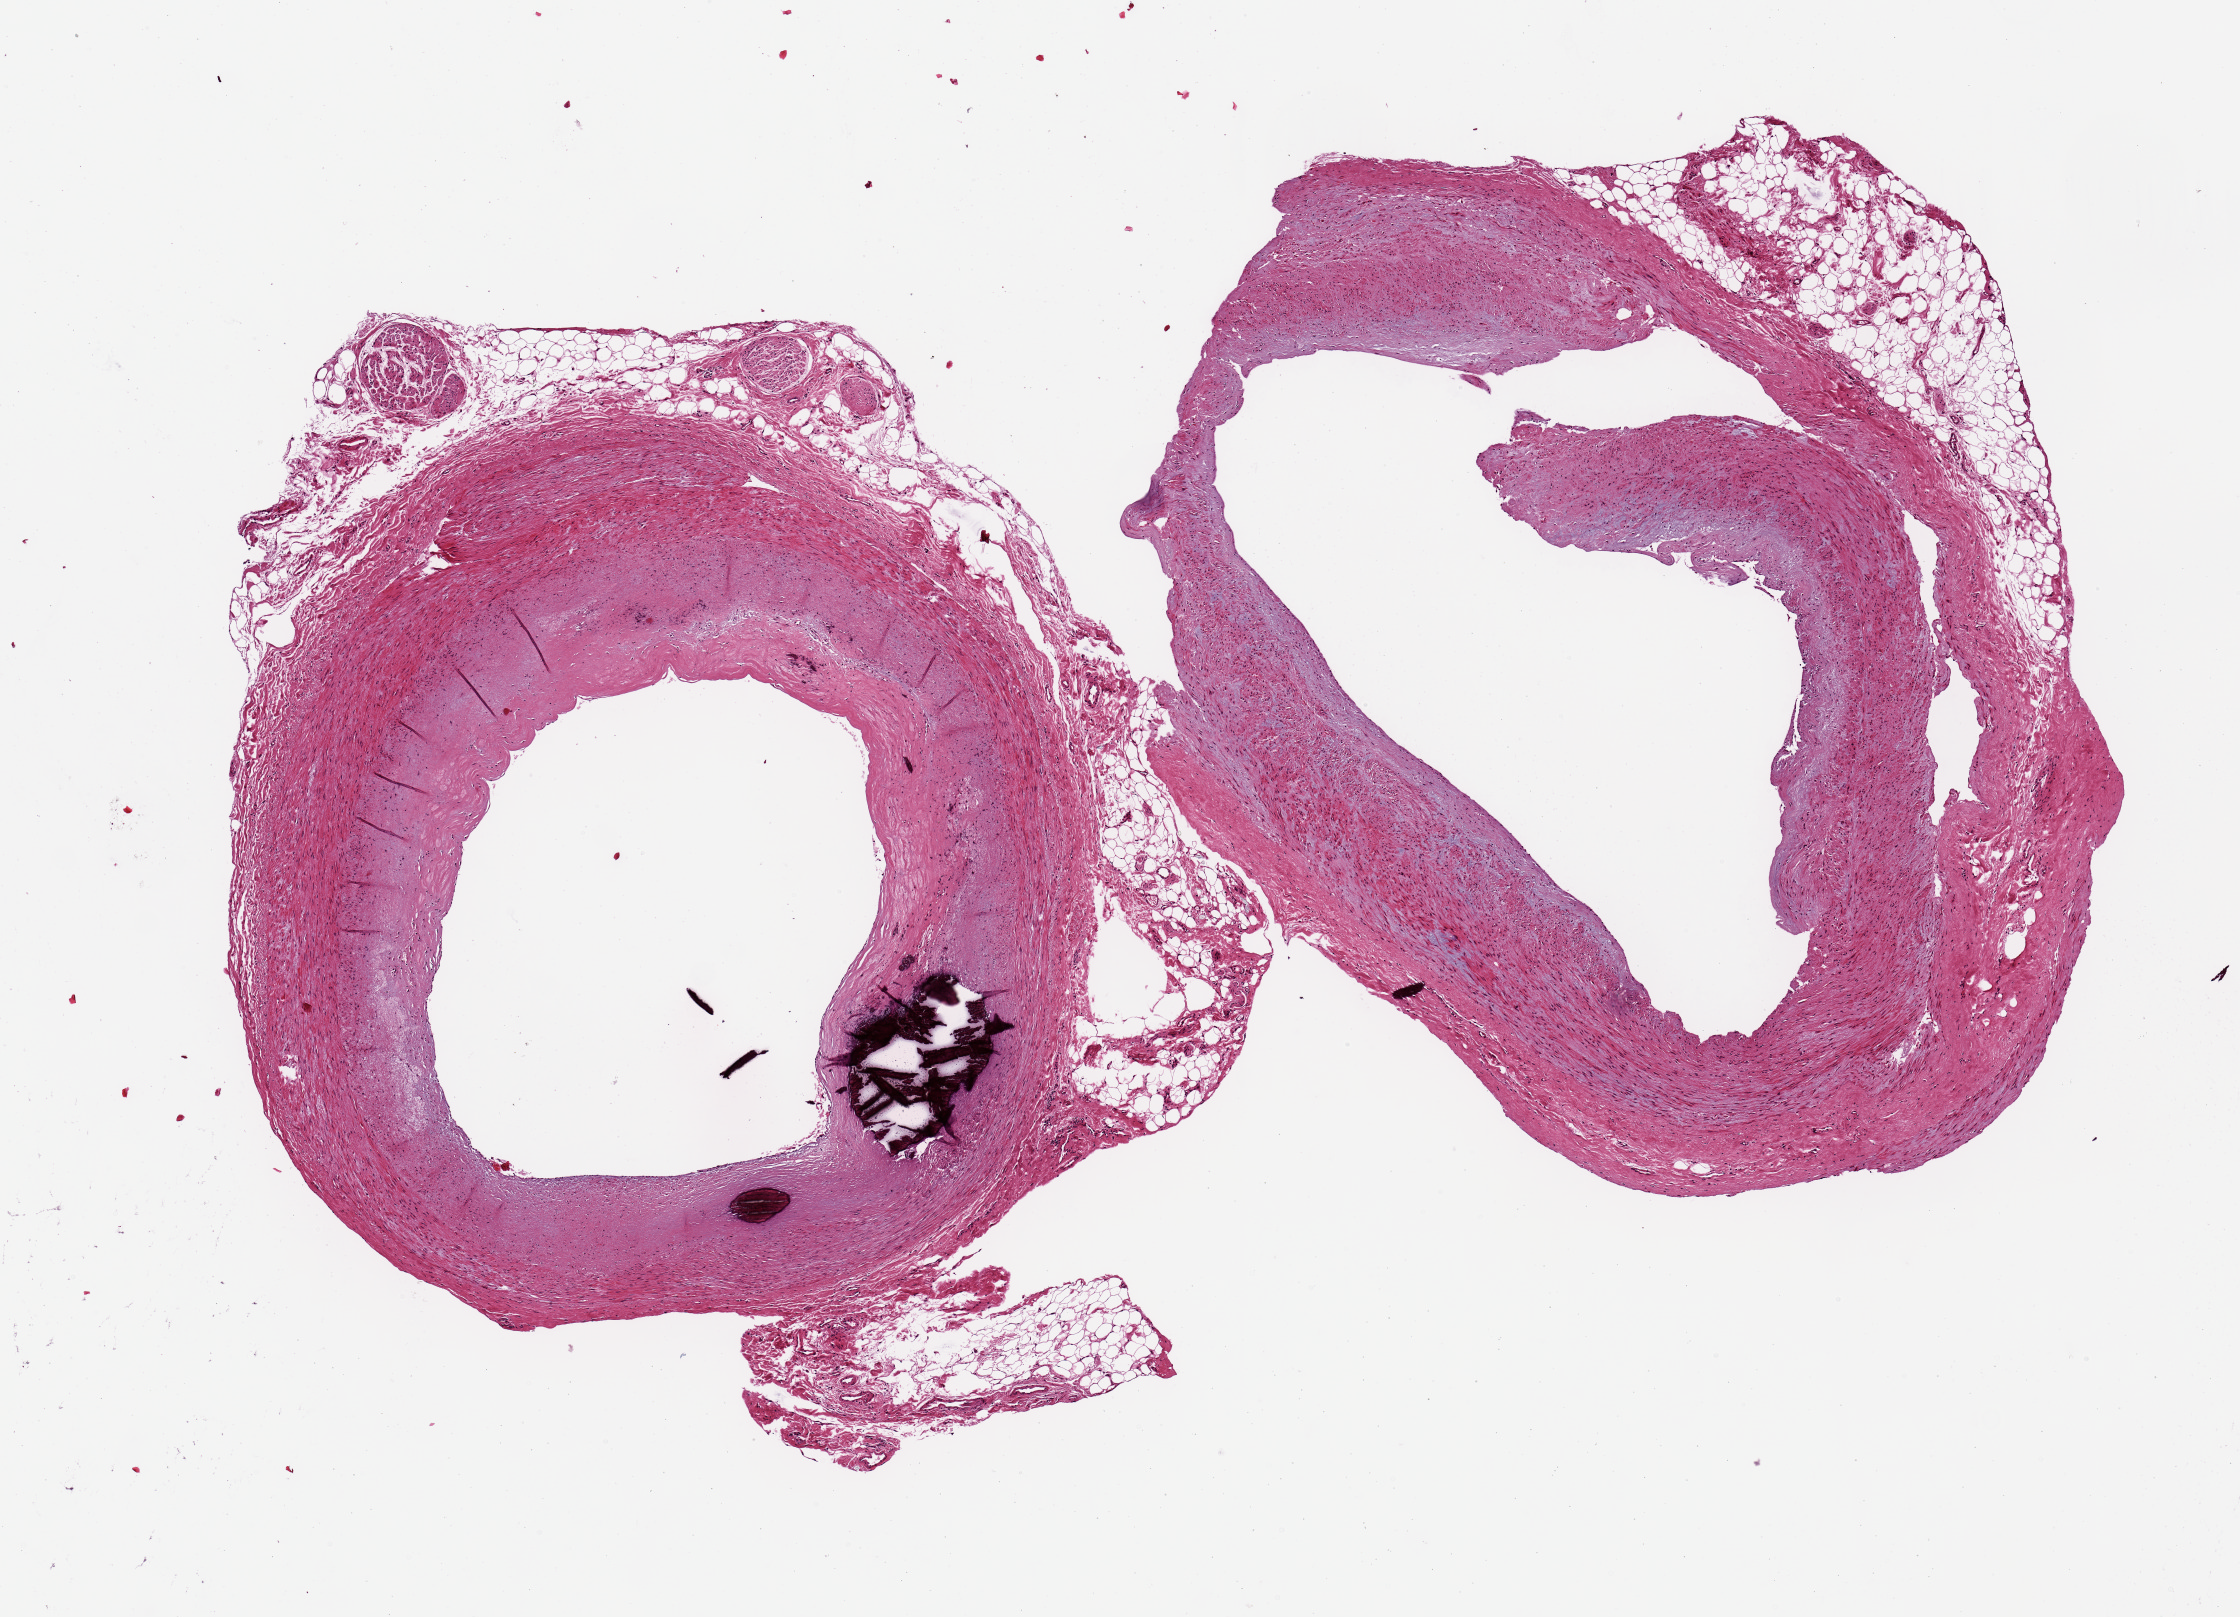
Digitized haematoxylin and eosin-stained section, a low-resolution overview of the entire scanned area, about 8.9 x 6.4 mm, PAXgene-fixed paraffin-embedded (PFPE) section, target tissue: coronary artery, donor tissue sample. Donor sex: female.
Reviewer comment on this tissue sample: Moderate calcified atherosclerosis, wide lumen.